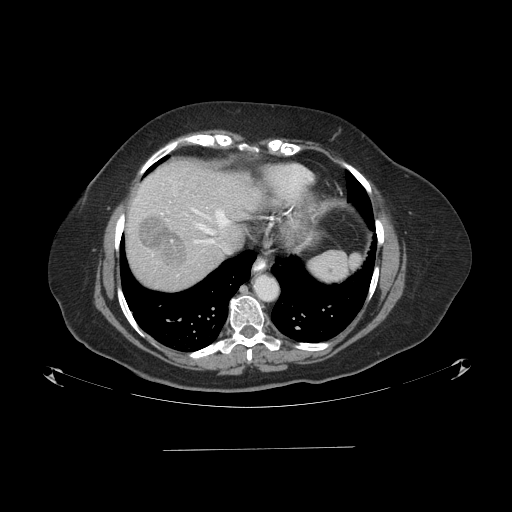
Contrast-enhanced abdominal CT (liver protocol), one axial slice. Slice 77 of 103 in the series (ordered by position). One of 2 acquisitions stored at this slice position. Soft-tissue window (W 400 / L 40 HU). 2.5 mm slice thickness. 512 × 512 image matrix, field of view 500 × 500 mm. Case-level facts recorded for this patient, not image findings: diagnosis: hepatocellular carcinoma (patient treated with transarterial chemoembolisation; whether this scan precedes or follows treatment is not stated here); TNM stage (as recorded): Stage-IIIA; Child-Pugh class: A; tumour differentiation: poorly differentiated; tumour nodularity: multinodular.
Annotated regions visible in this slice (semi-automatic segmentation, software-assisted and operator-edited):
- liver parenchyma outside the tumour (the mass and vessels are separate outlines, so this box may not span the whole liver): box from (x=126, y=158) to (x=262, y=290) px
- mass: (x=137, y=215)–(x=187, y=268)
- liver vessels: (x=191, y=208)–(x=230, y=244)